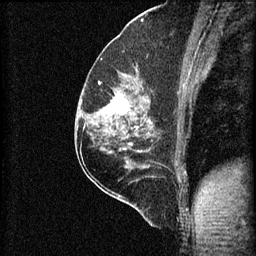
Breast MRI (dynamic contrast-enhanced), one sagittal slice; position 36 of 60 along the scan axis; 3 images stored at this slice position (order not interpretable as contrast timing); 1.5 T; TE 4.2 ms, TR 8.2 ms; 2 mm slice thickness; 256 × 256 image matrix, field of view 180 × 180 mm. Female patient, age 59 years.
Outlined on this slice (semi-automatic segmentation, software-assisted and operator-edited):
- analysis volume of interest (the breast-tissue region the enhancement analysis was run in; not a lesion): bounding box (x1, y1, x2, y2) in pixels: (92, 74, 154, 131)
- tumour enhancement mask (voxels above the 70 % enhancement threshold inside the analysis volume of interest): (99, 82, 150, 115)